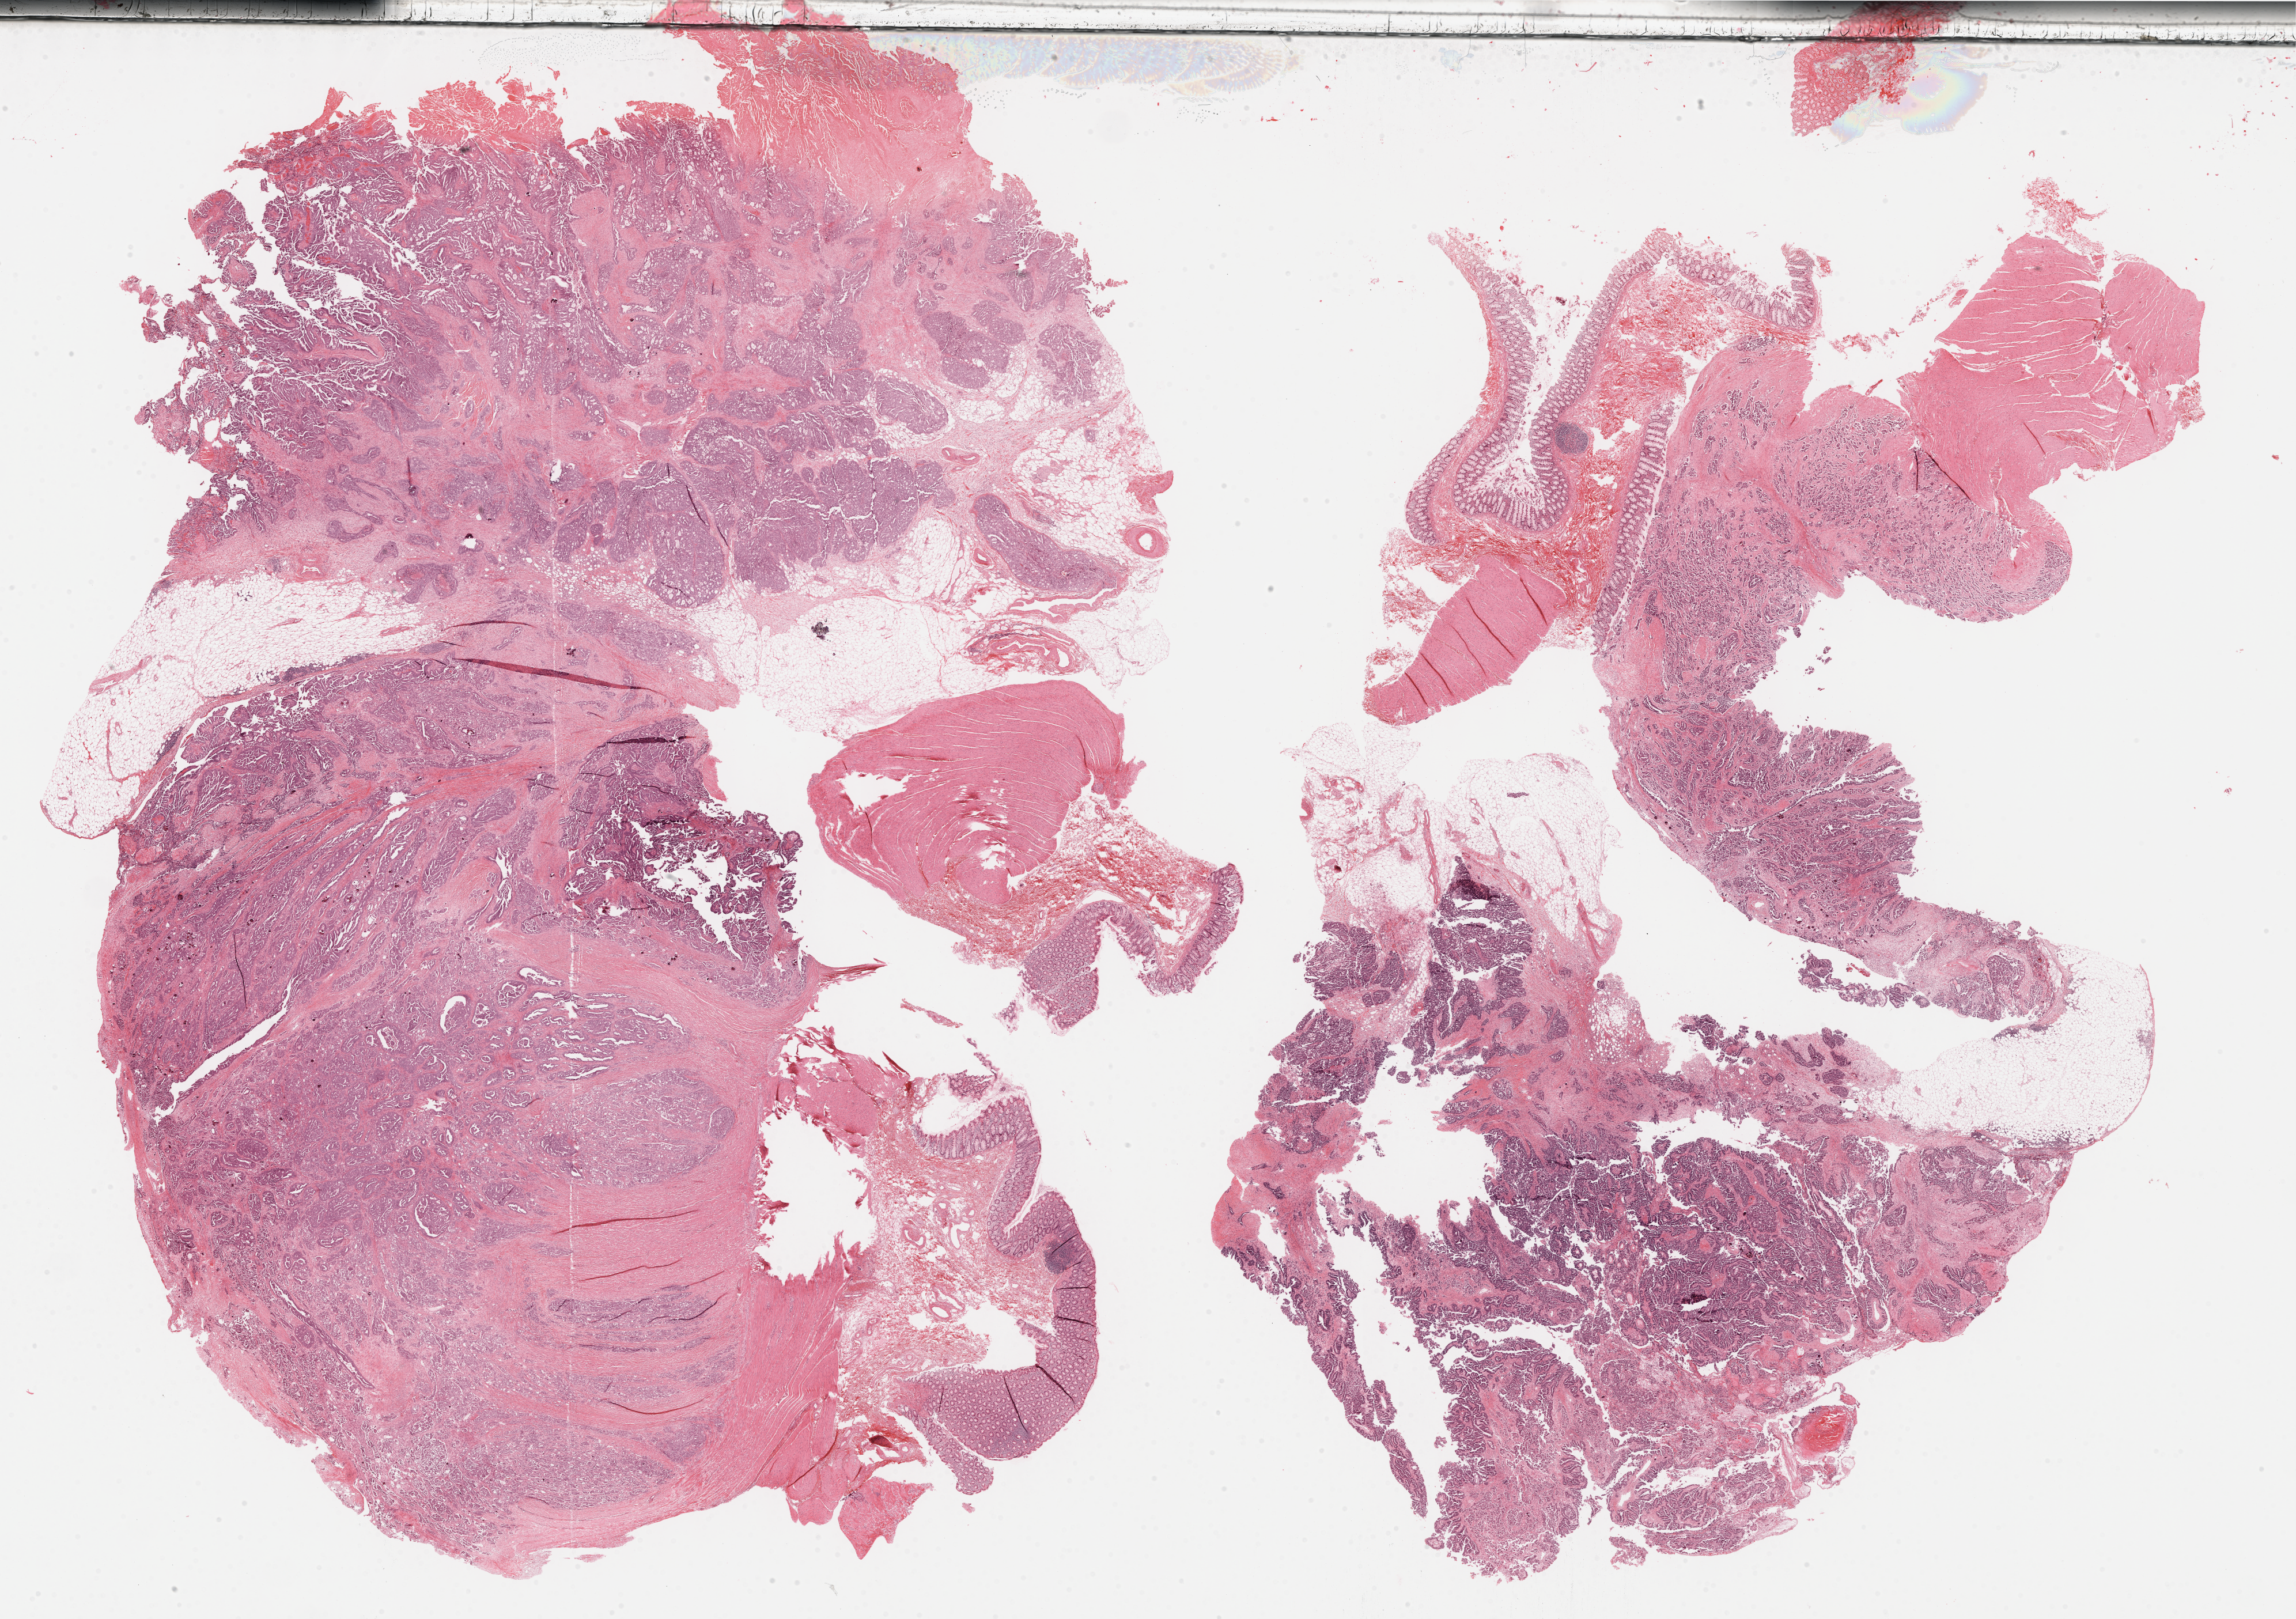
Whole-slide histology image, H&E-stained — low-resolution overview of the scanned area, about 32.2 x 22.7 mm (slide scanned at 40x); FFPE section; ovary, primary tumour sample. Female, age 65 years at initial diagnosis. Histologic grade: G3 (poorly differentiated).
FIGO stage: IIIC. Laterality: bilateral. Diagnosis: Serous cystadenocarcinoma, NOS.